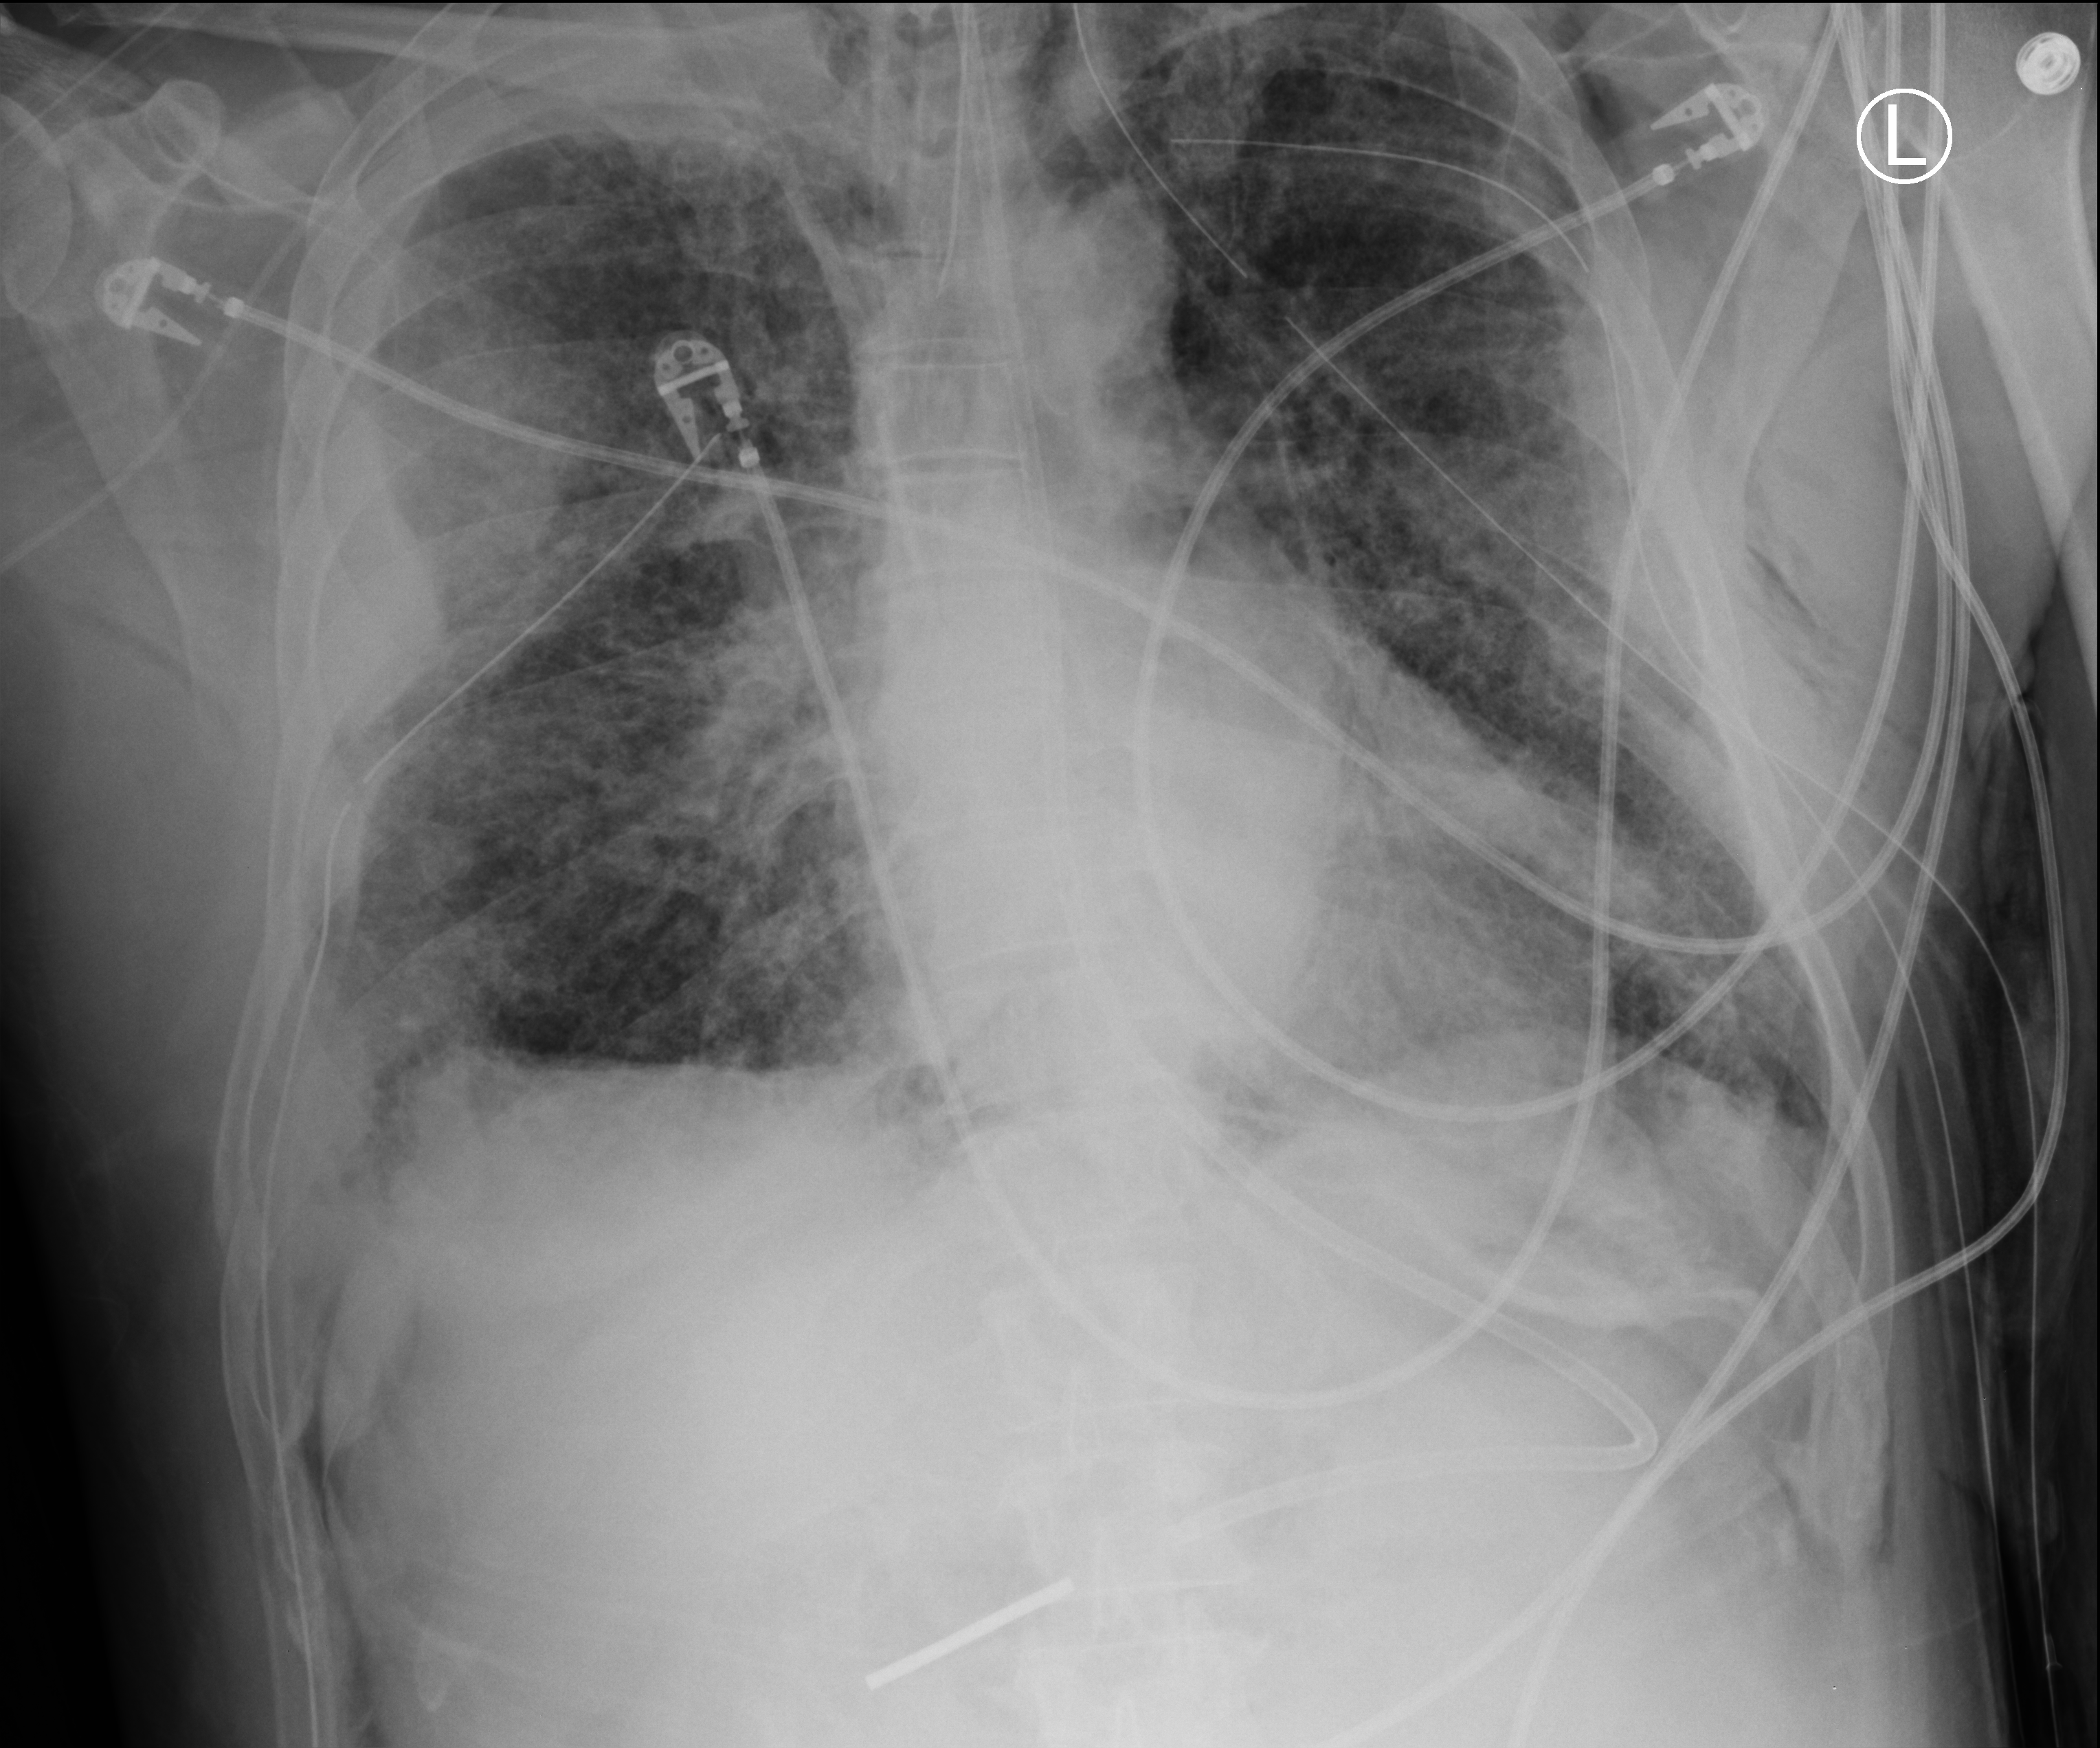
Chest X-ray (portable). Patient hospitalised with COVID-19; male, aged 18–59 years.
Admission-level facts for this patient (not findings on this image; timing relative to this image not recorded): mechanically ventilated during this hospital stay: yes; other chronic lung disease (admission record): no.